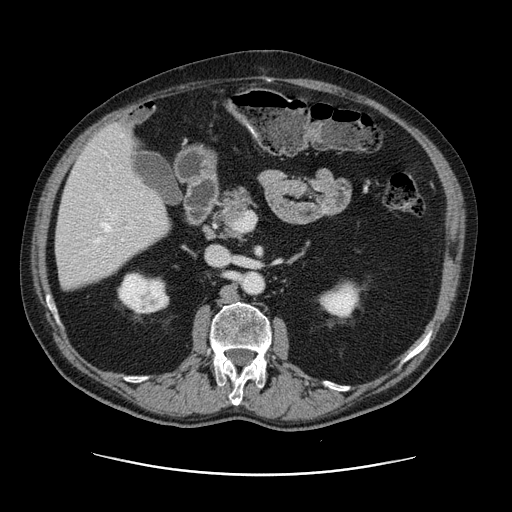
Contrast-enhanced abdominal CT, one axial slice. Slice 60 of 141 in the series (ordered by position). 120 kVp. Intravenous contrast given. Soft-tissue window (W 400 / L 40 HU). 2.5 mm slice thickness. 512 × 512 image matrix, field of view 395 × 395 mm. Male patient, age 72 years. Case-level facts recorded for this patient, not image findings: diagnosis: colorectal cancer liver metastases, imaged before liver resection; multiple liver metastases: yes; largest metastasis: 5.4 cm; disease in both lobes: yes.
Annotated regions visible in this slice (outlined manually by an expert reader):
- hepatic veins: box from (x=95, y=135) to (x=123, y=243) px
- liver: (x=57, y=125)–(x=170, y=290)
- planned liver remnant (the part of the liver to remain after resection): (x=57, y=184)–(x=170, y=290)
- portal vein (with intrahepatic branches): (x=99, y=220)–(x=137, y=239)